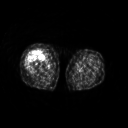
FDG PET of an extremity soft-tissue mass (from a PET/CT study), one axial slice. Position 226 of 311 along the scan axis. 3.27 mm slice thickness. 128 × 128 image matrix. Patient: female, 57 years. From the clinical record (not read from this slice): histological type: pleiomorphic undifferentiated sarcoma; grade: high; site of the primary tumour: right quadricep.
Structures marked on this image (expert contour drawn on MRI and transferred to this co-registered scan by the dataset authors):
- tumour plus oedema (research contour): bounding box <26,50,42,69> (left, top, right, bottom; pixels)